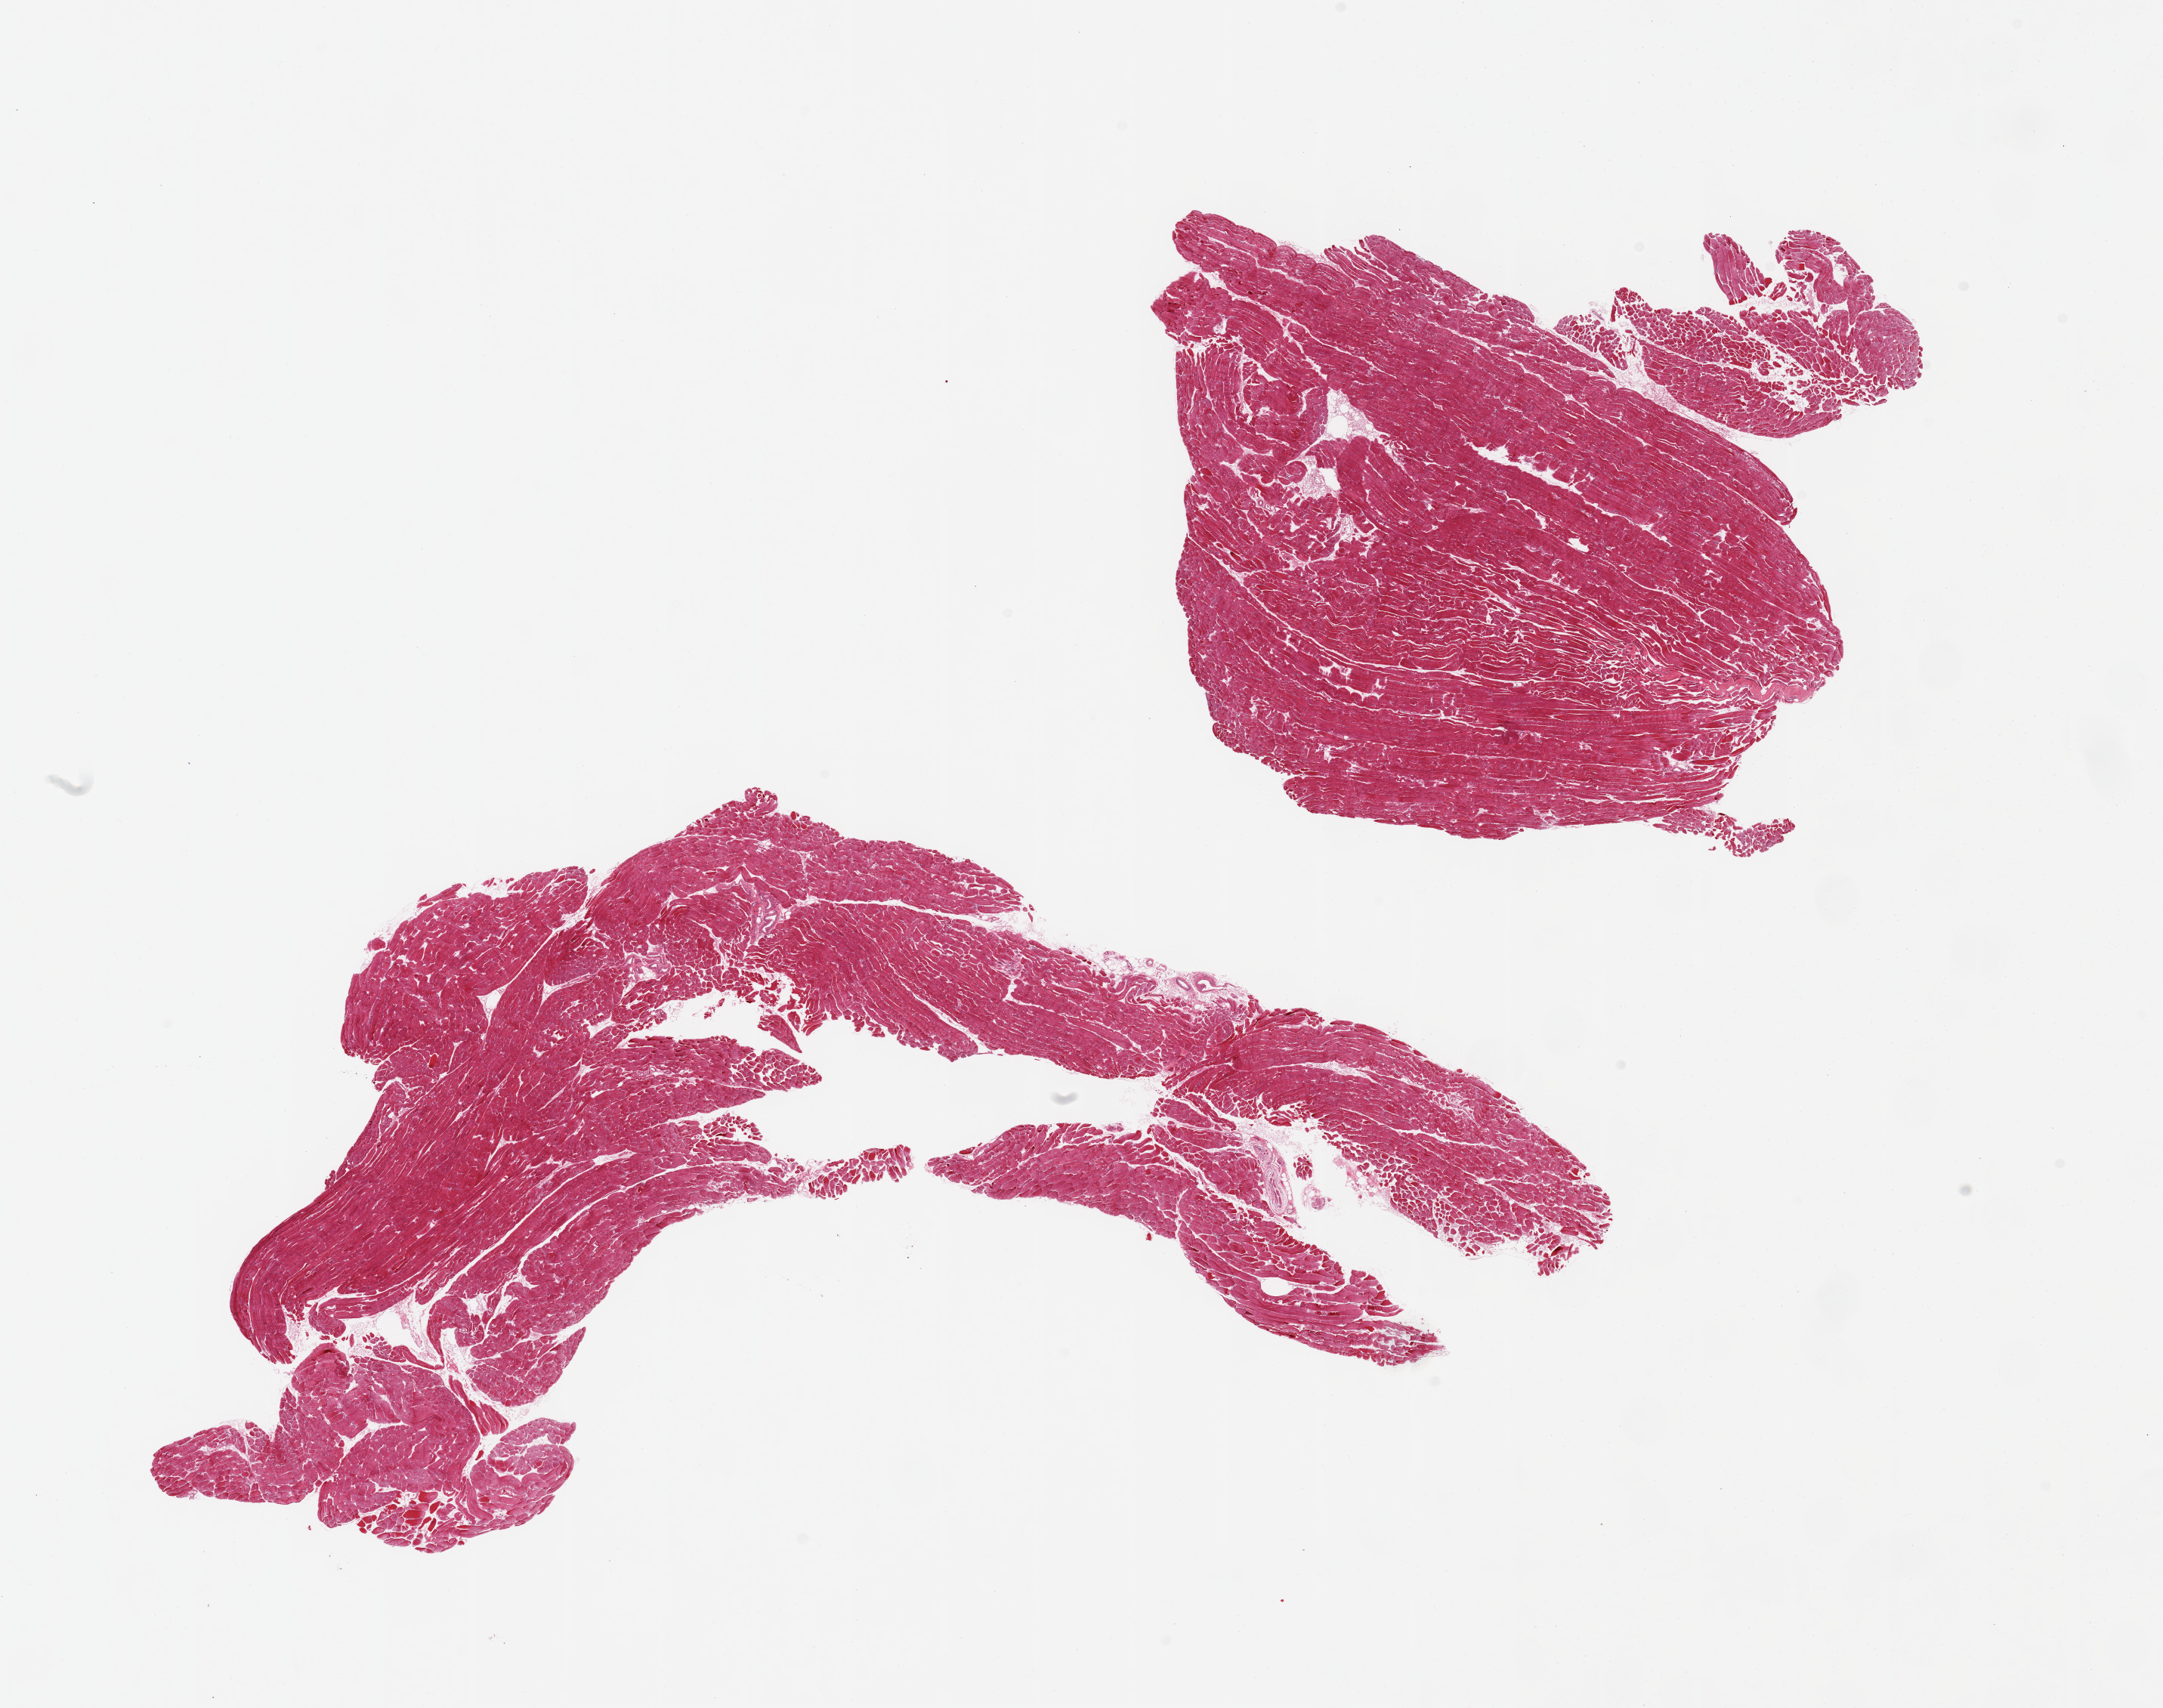
Whole-slide image, H&E stain, a low-resolution overview of the entire scanned area, about 22.6 x 17.9 mm (from a 20x scan). PAXgene-fixed paraffin-embedded (PFPE) section. Target tissue: skeletal muscle. Tissue donor sample. Donor: male.
* pathologist's review note for this sample: 2 pieces, minimal interstitial fat